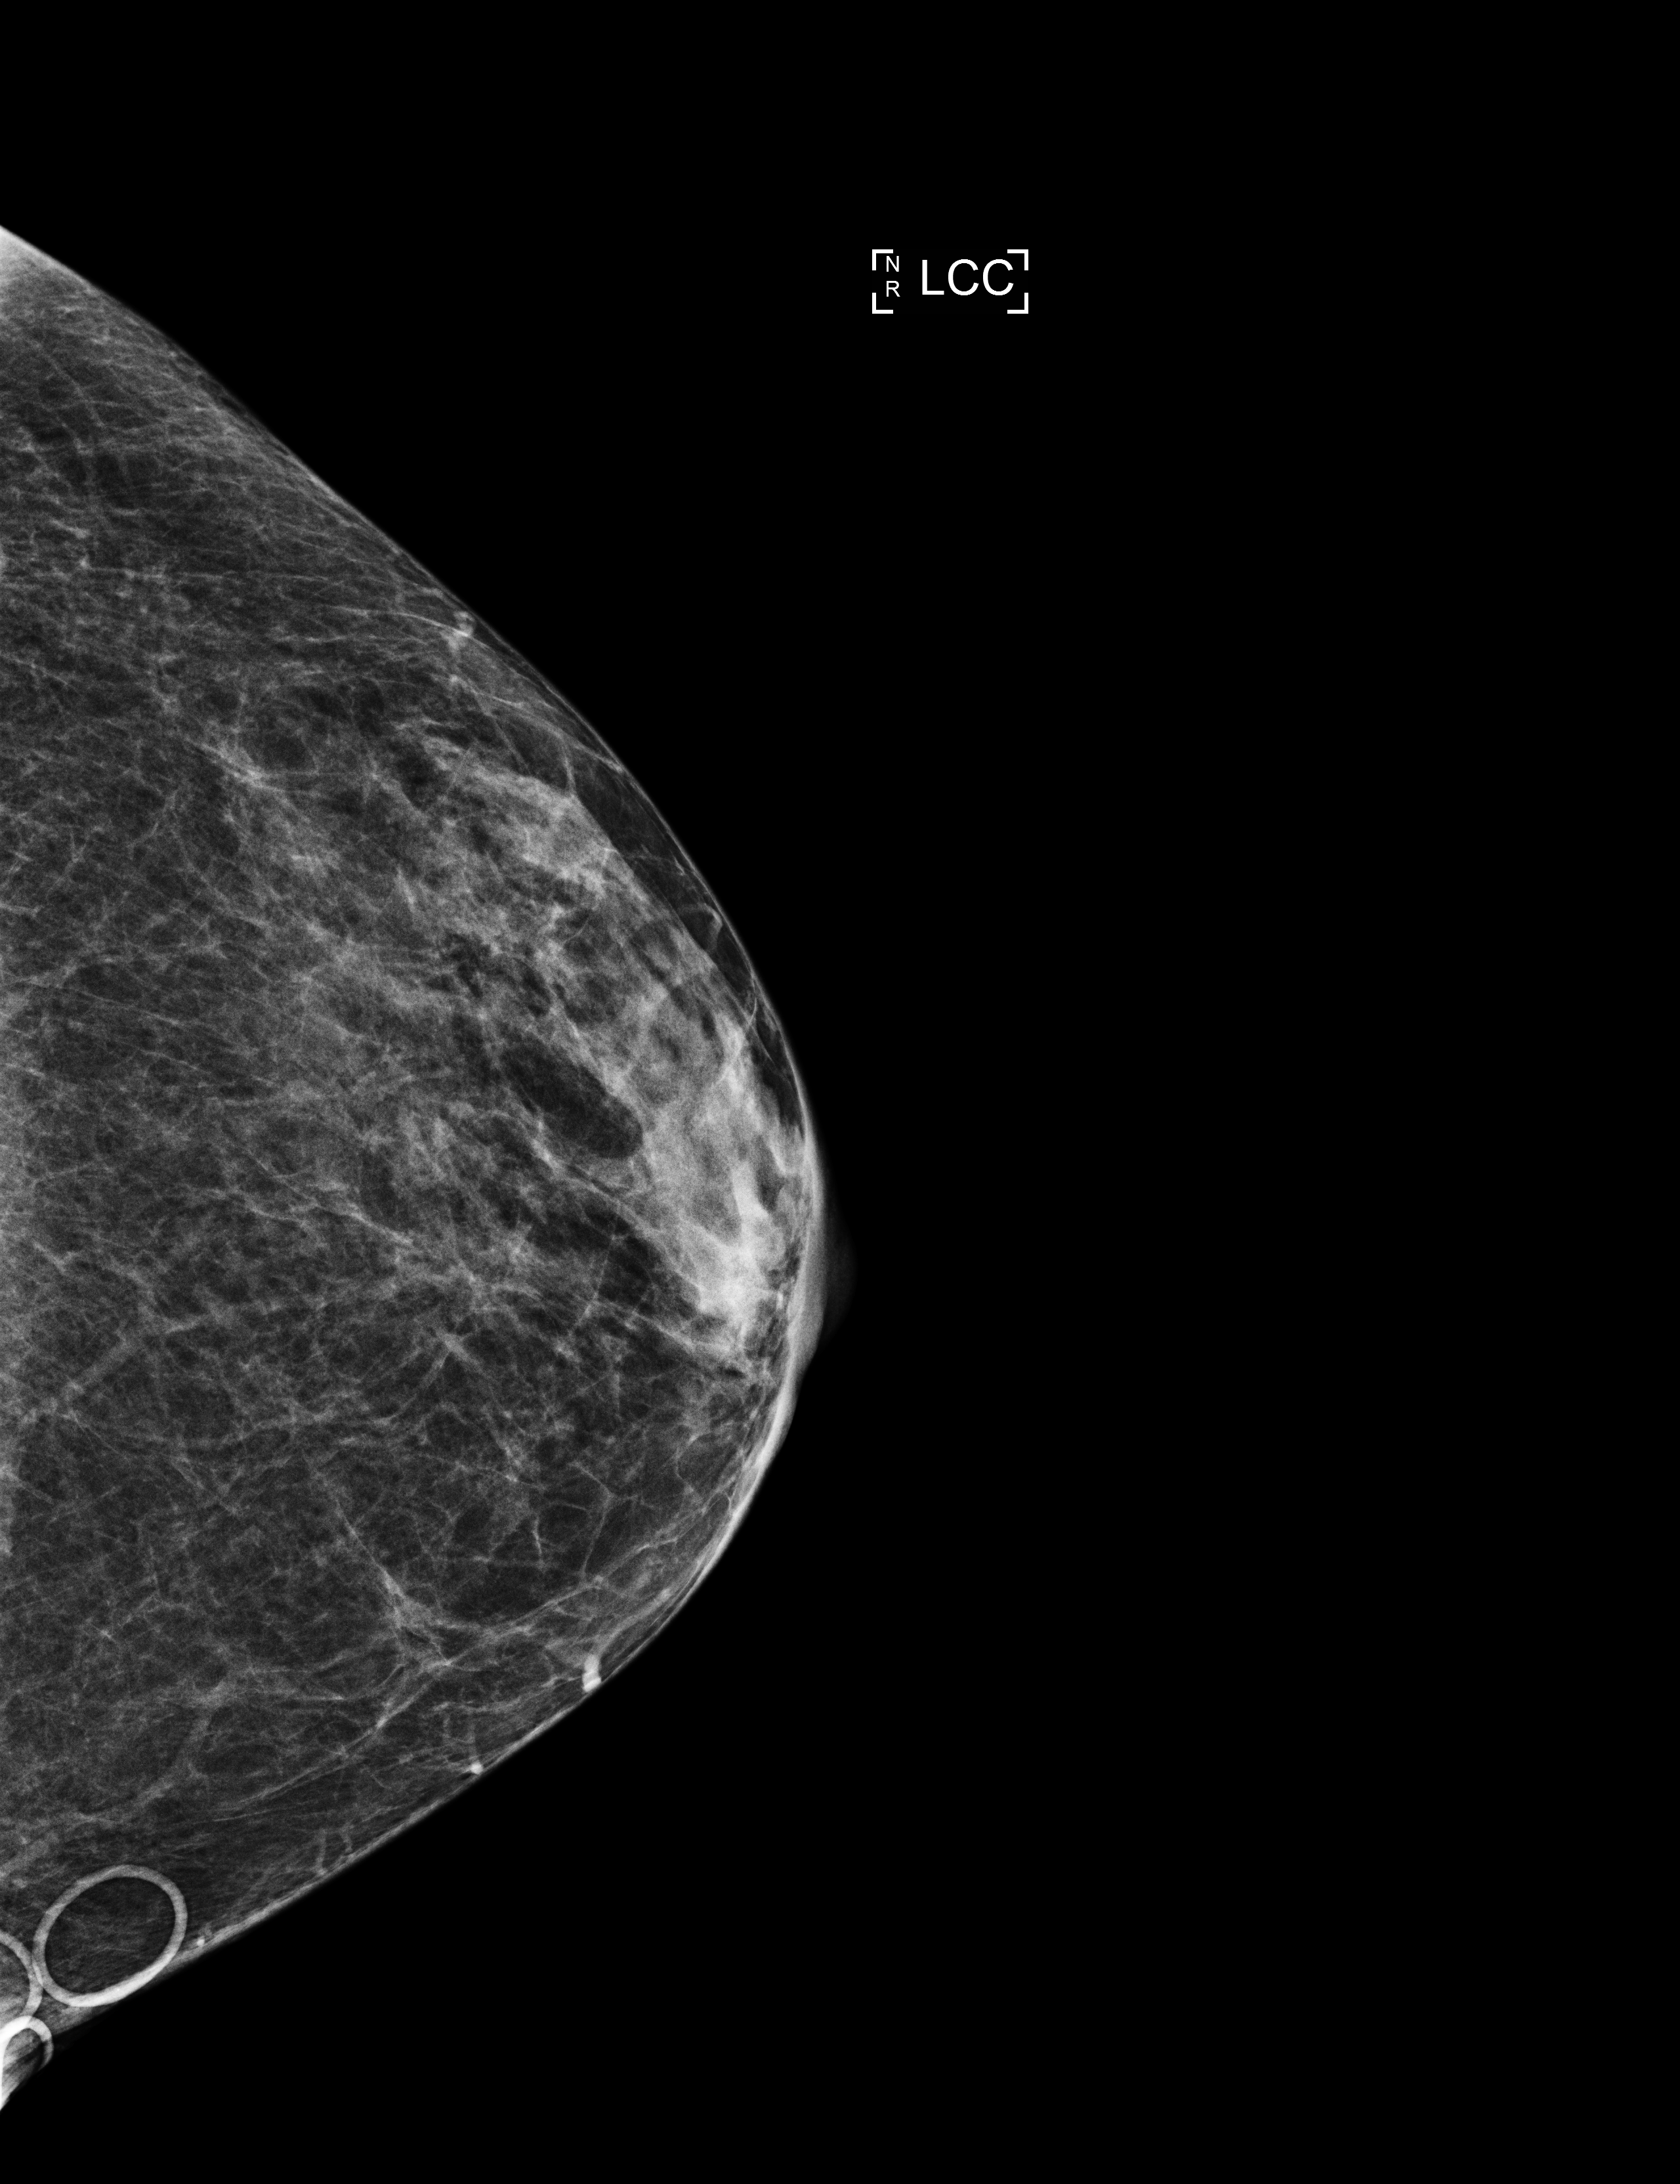
Full-field digital mammogram (FFDM), left breast, craniocaudal (CC) view, annual screening mammography examination, compressed breast thickness 29 mm, system: Selenia Dimensions. Patient: female, 59 years.
Breast density at the screening exam (both breasts): scattered fibroglandular densities (BI-RADS density category b). Final BI-RADS assessment for this screening round (tomosynthesis exam, both breasts): category 1. Recall: no recall after this screen.